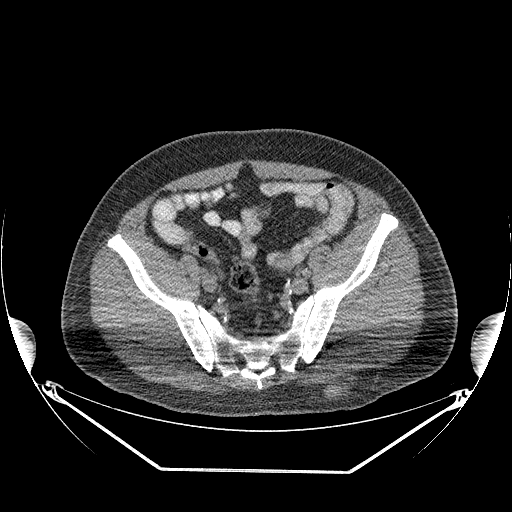
CT of an extremity soft-tissue mass (from a PET/CT study), one axial slice. Position 81 of 267 along the scan axis. Reconstruction kernel STANDARD. Soft-tissue window (W 400 / L 40 HU). 3.75 mm slice thickness. 512 × 512 image matrix. Male patient. From the clinical record (not read from this slice): histological type: pleiomorphic leiomyosarcoma; grade: high; site of the primary tumour: left buttock.
Structures marked on this image (expert contour drawn on MRI and transferred to this co-registered scan by the dataset authors):
- gross tumour volume including surrounding oedema: bounding box (x1, y1, x2, y2) in pixels: (343, 379, 353, 394)
- gross tumour volume (mass): (345, 384, 352, 394)